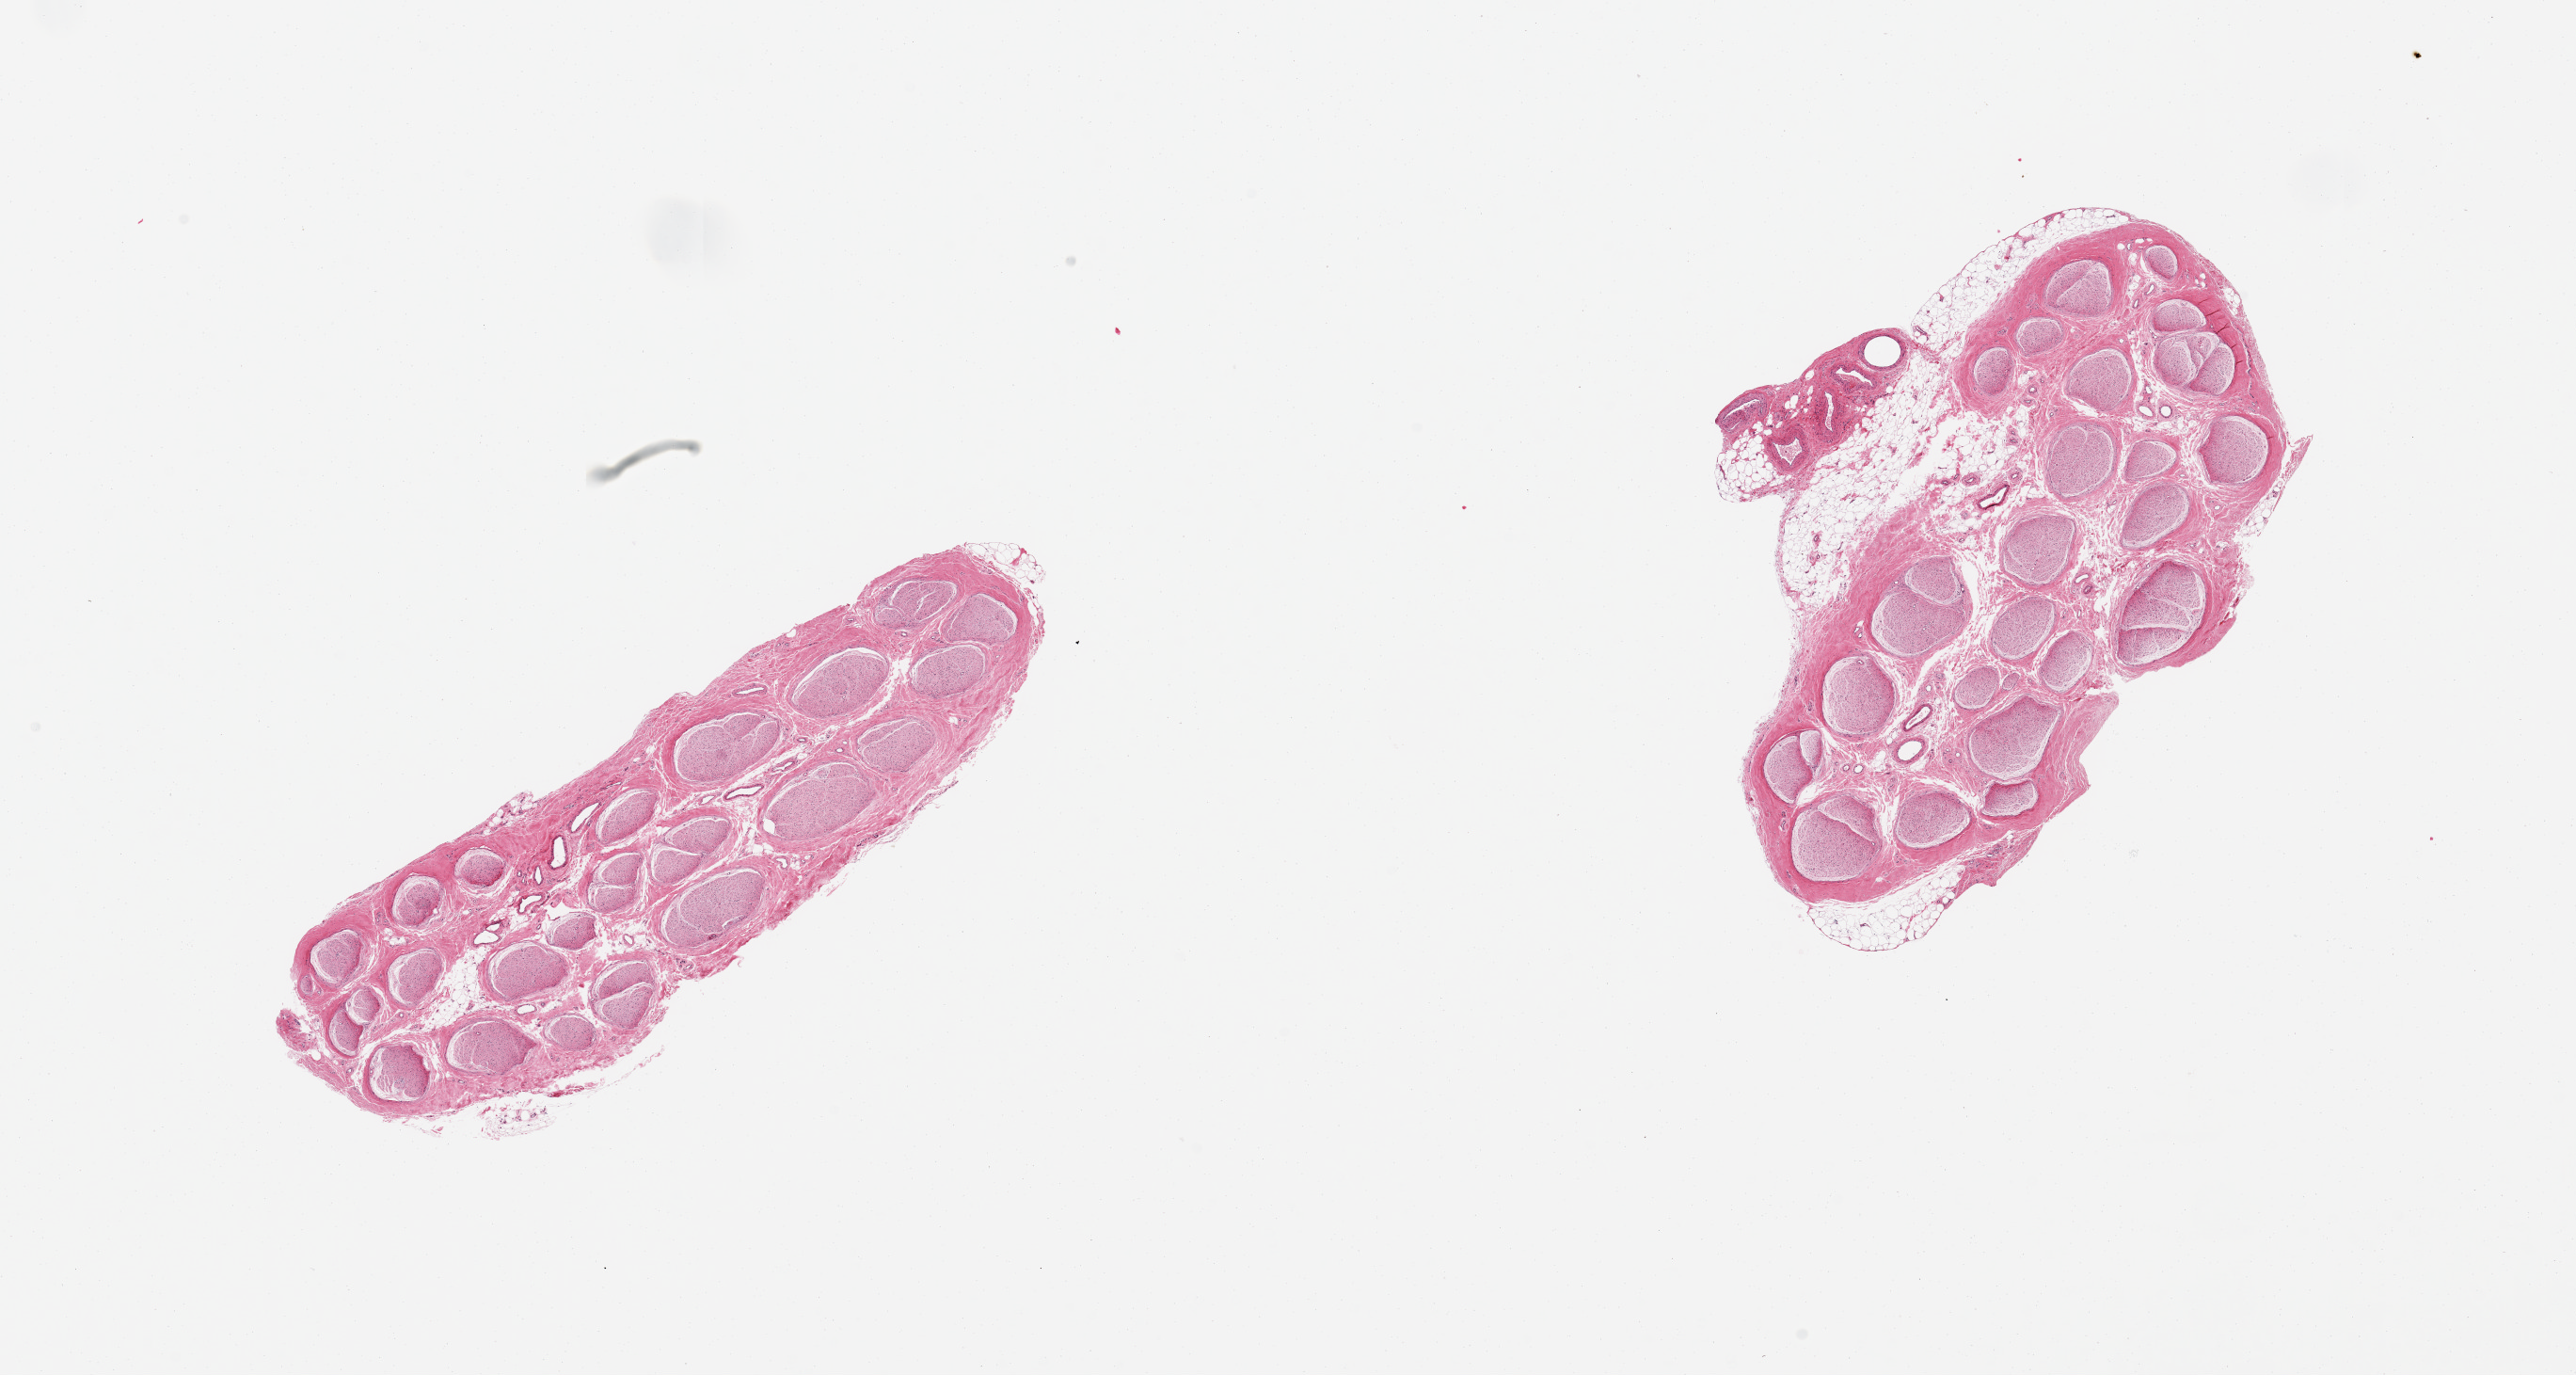
Hematoxylin and eosin (H&E) whole-slide image — a low-resolution overview of the entire scanned area, about 21.7 x 11.6 mm. PAXgene-fixed paraffin-embedded (PFPE) section. Sampled site (target tissue): tibial nerve. Donor tissue sample. Donor sex: male.
• pathologist's review note for this sample: 2 pieces, nubbin of adherent fat/vascular elements up to ~1mm